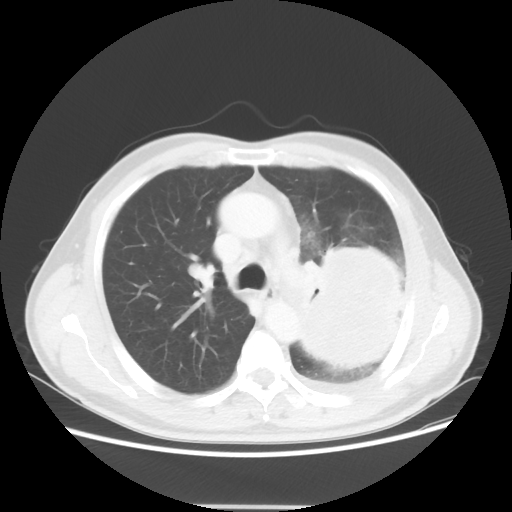
Chest CT, one axial slice. 100 kVp. Lung window (W 1500 / L -600 HU). 512 × 512 image matrix, field of view 391 × 391 mm. Male patient, age 60 years. Case-level facts recorded for this patient, not image findings: clinical TNM (as recorded): T4 N1 M1a; histopathological grade: G3.
Annotated regions visible in this slice (bounding box drawn by a radiologist):
- lung tumour (recorded histology: large cell carcinoma): bounding box [x1, y1, x2, y2] px = [288, 232, 410, 381]